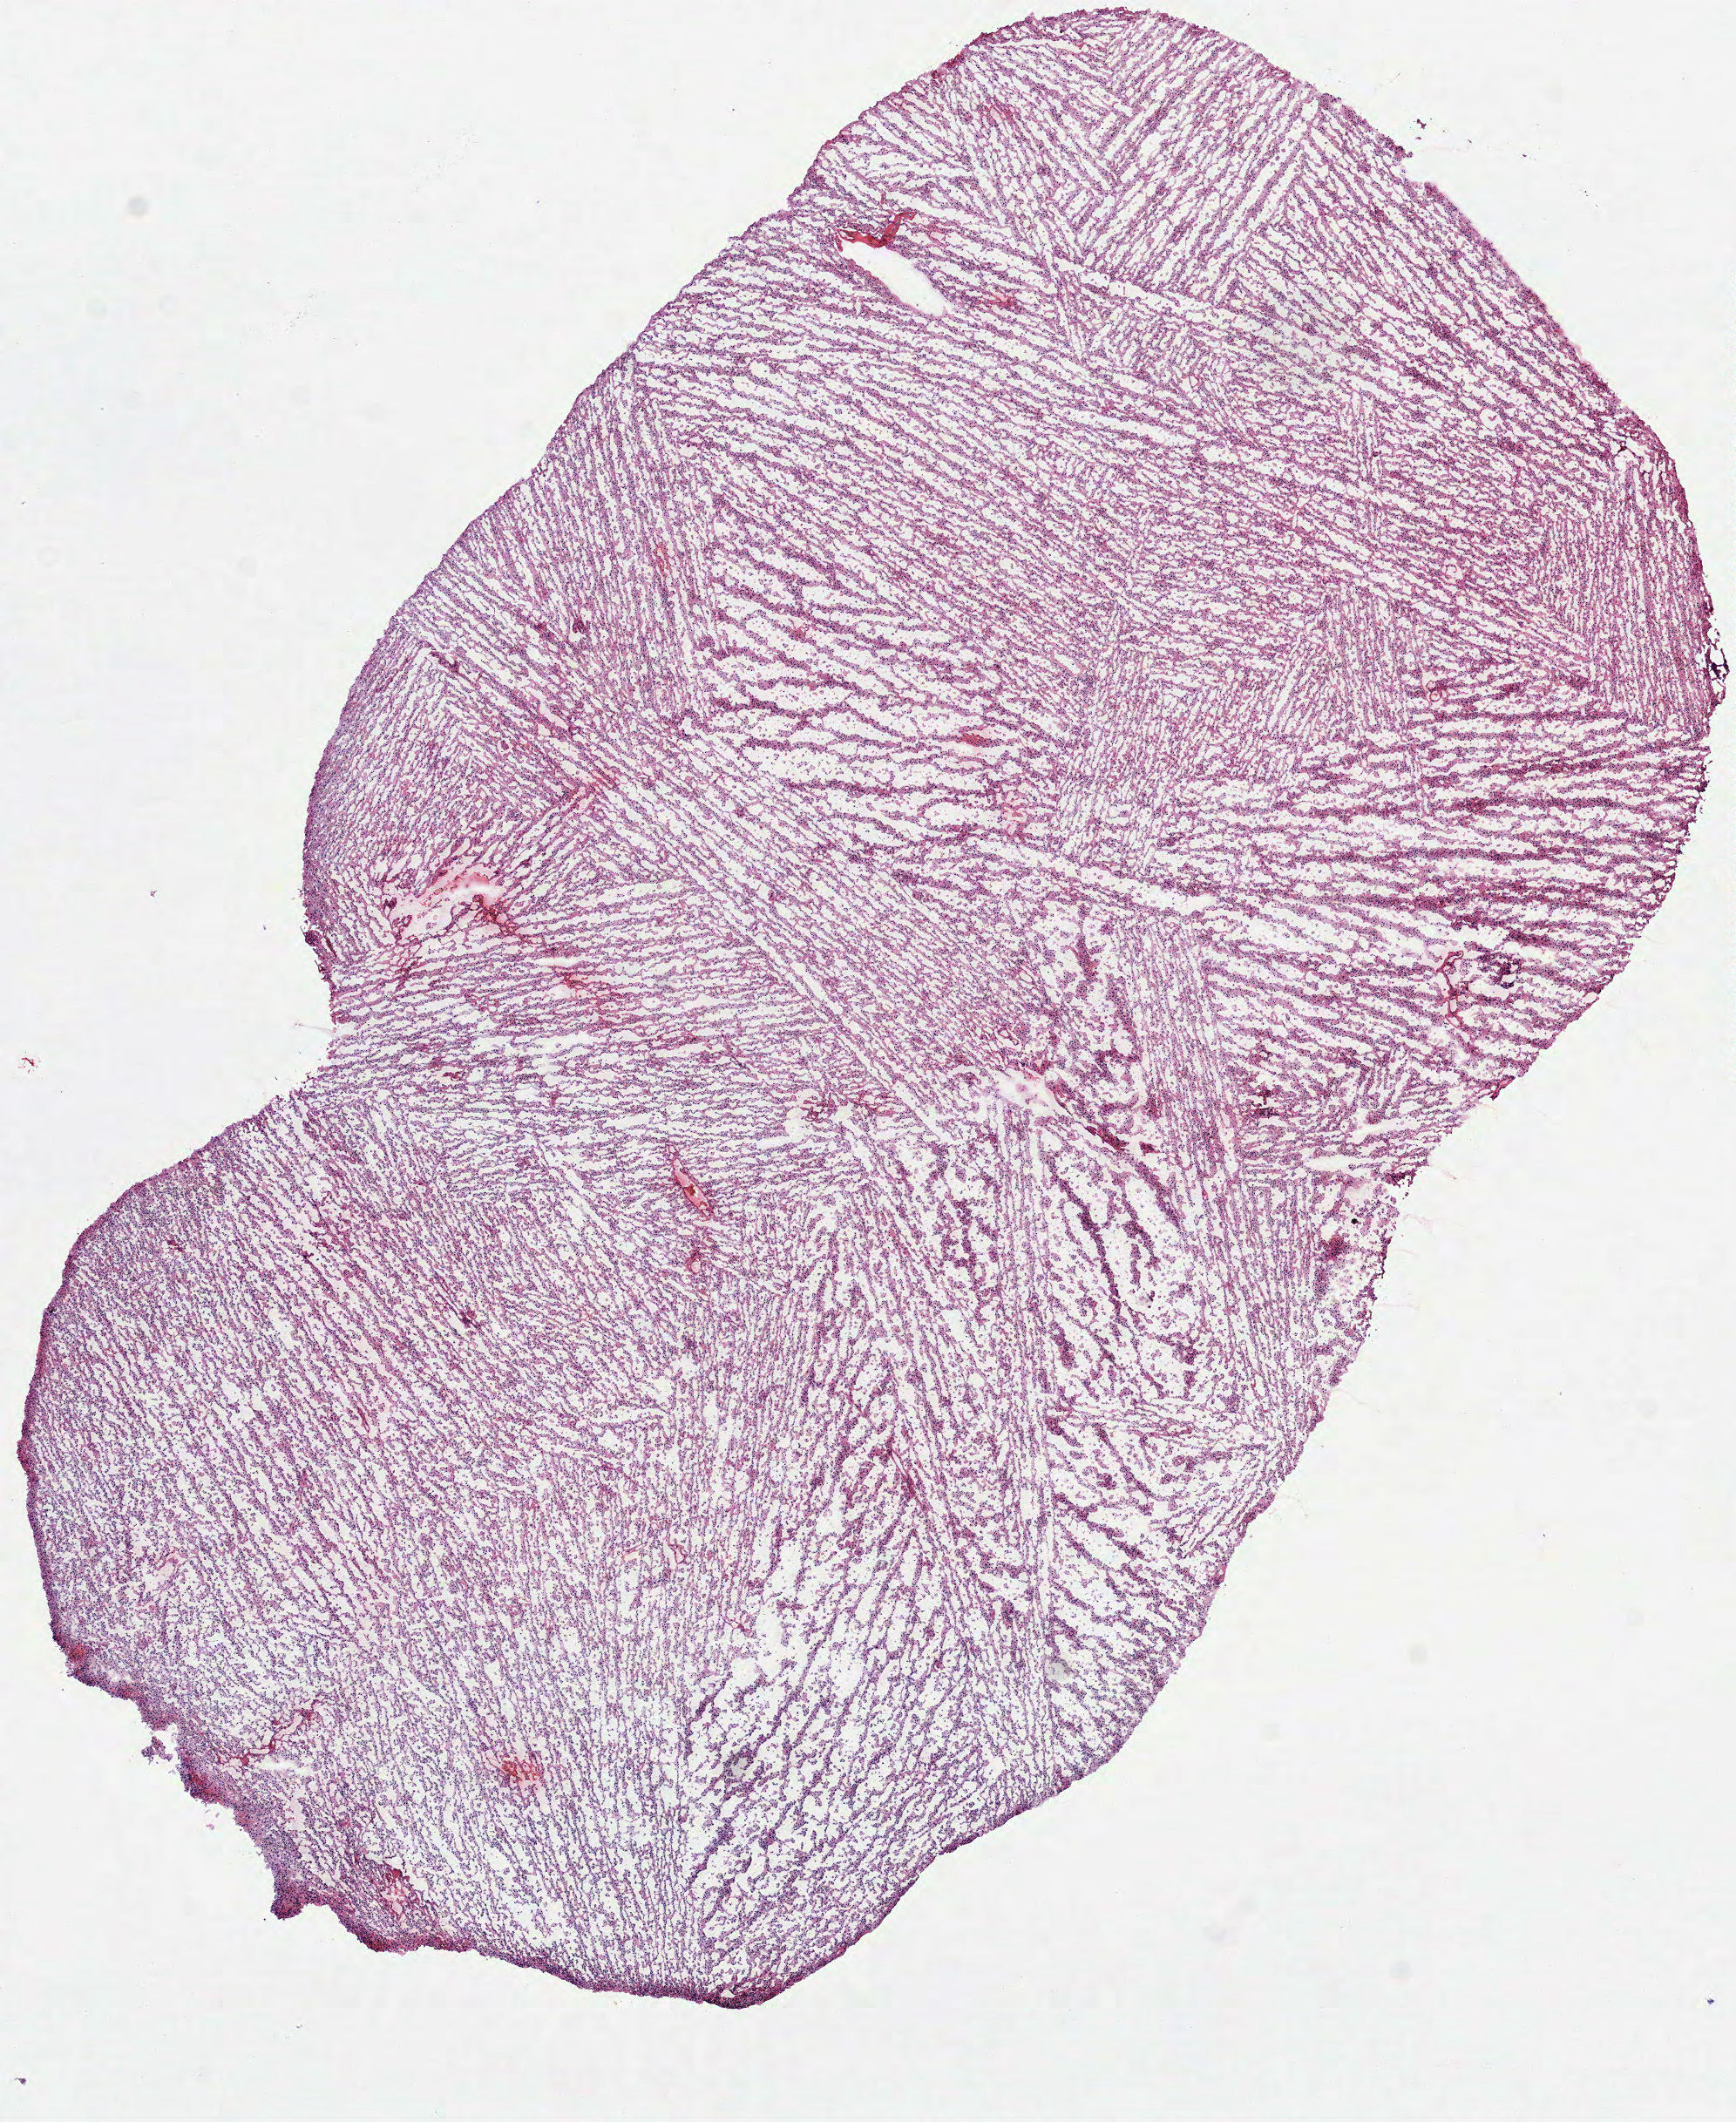
Digitized Hematoxylin and eosin (H&E) stained tissue section (whole slide) — whole scanned area (about 8.0 x 9.8 mm, acquisition: 40x scan) shown as a low-resolution overview, frozen section, sample: primary tumour, brain. Patient: female, age at initial diagnosis 57 years. Histologic grade: G2 (moderately differentiated). Pathologist review of this section (percent, as recorded): tumour cells 100%, tumour nuclei 80%, normal cells 0%, stromal cells 0%, necrosis 0%.
Pathologic diagnosis: Oligodendroglioma, NOS.